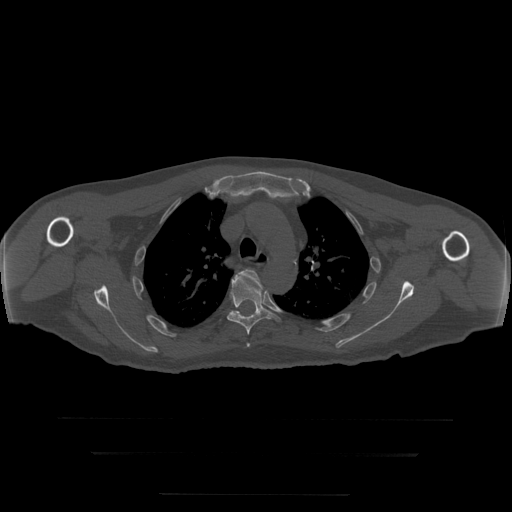
CT including the spine, one axial slice. Position 227 of 397 along the scan axis. 120 kVp. Bone window (W 1800 / L 400 HU). 1.25 mm slice thickness. 512 × 512 image matrix. Patient age 73 years. Case-level facts recorded for this patient, not image findings: primary cancer: prostate.
Annotated regions visible in this slice (semi-automatic segmentation, software-assisted and operator-edited):
- T4 vertebra: bounding box (x1, y1, x2, y2) in pixels: (238, 270, 263, 346)
- T5 vertebra: (227, 275, 280, 347)
- T6 vertebra: (232, 310, 240, 316)